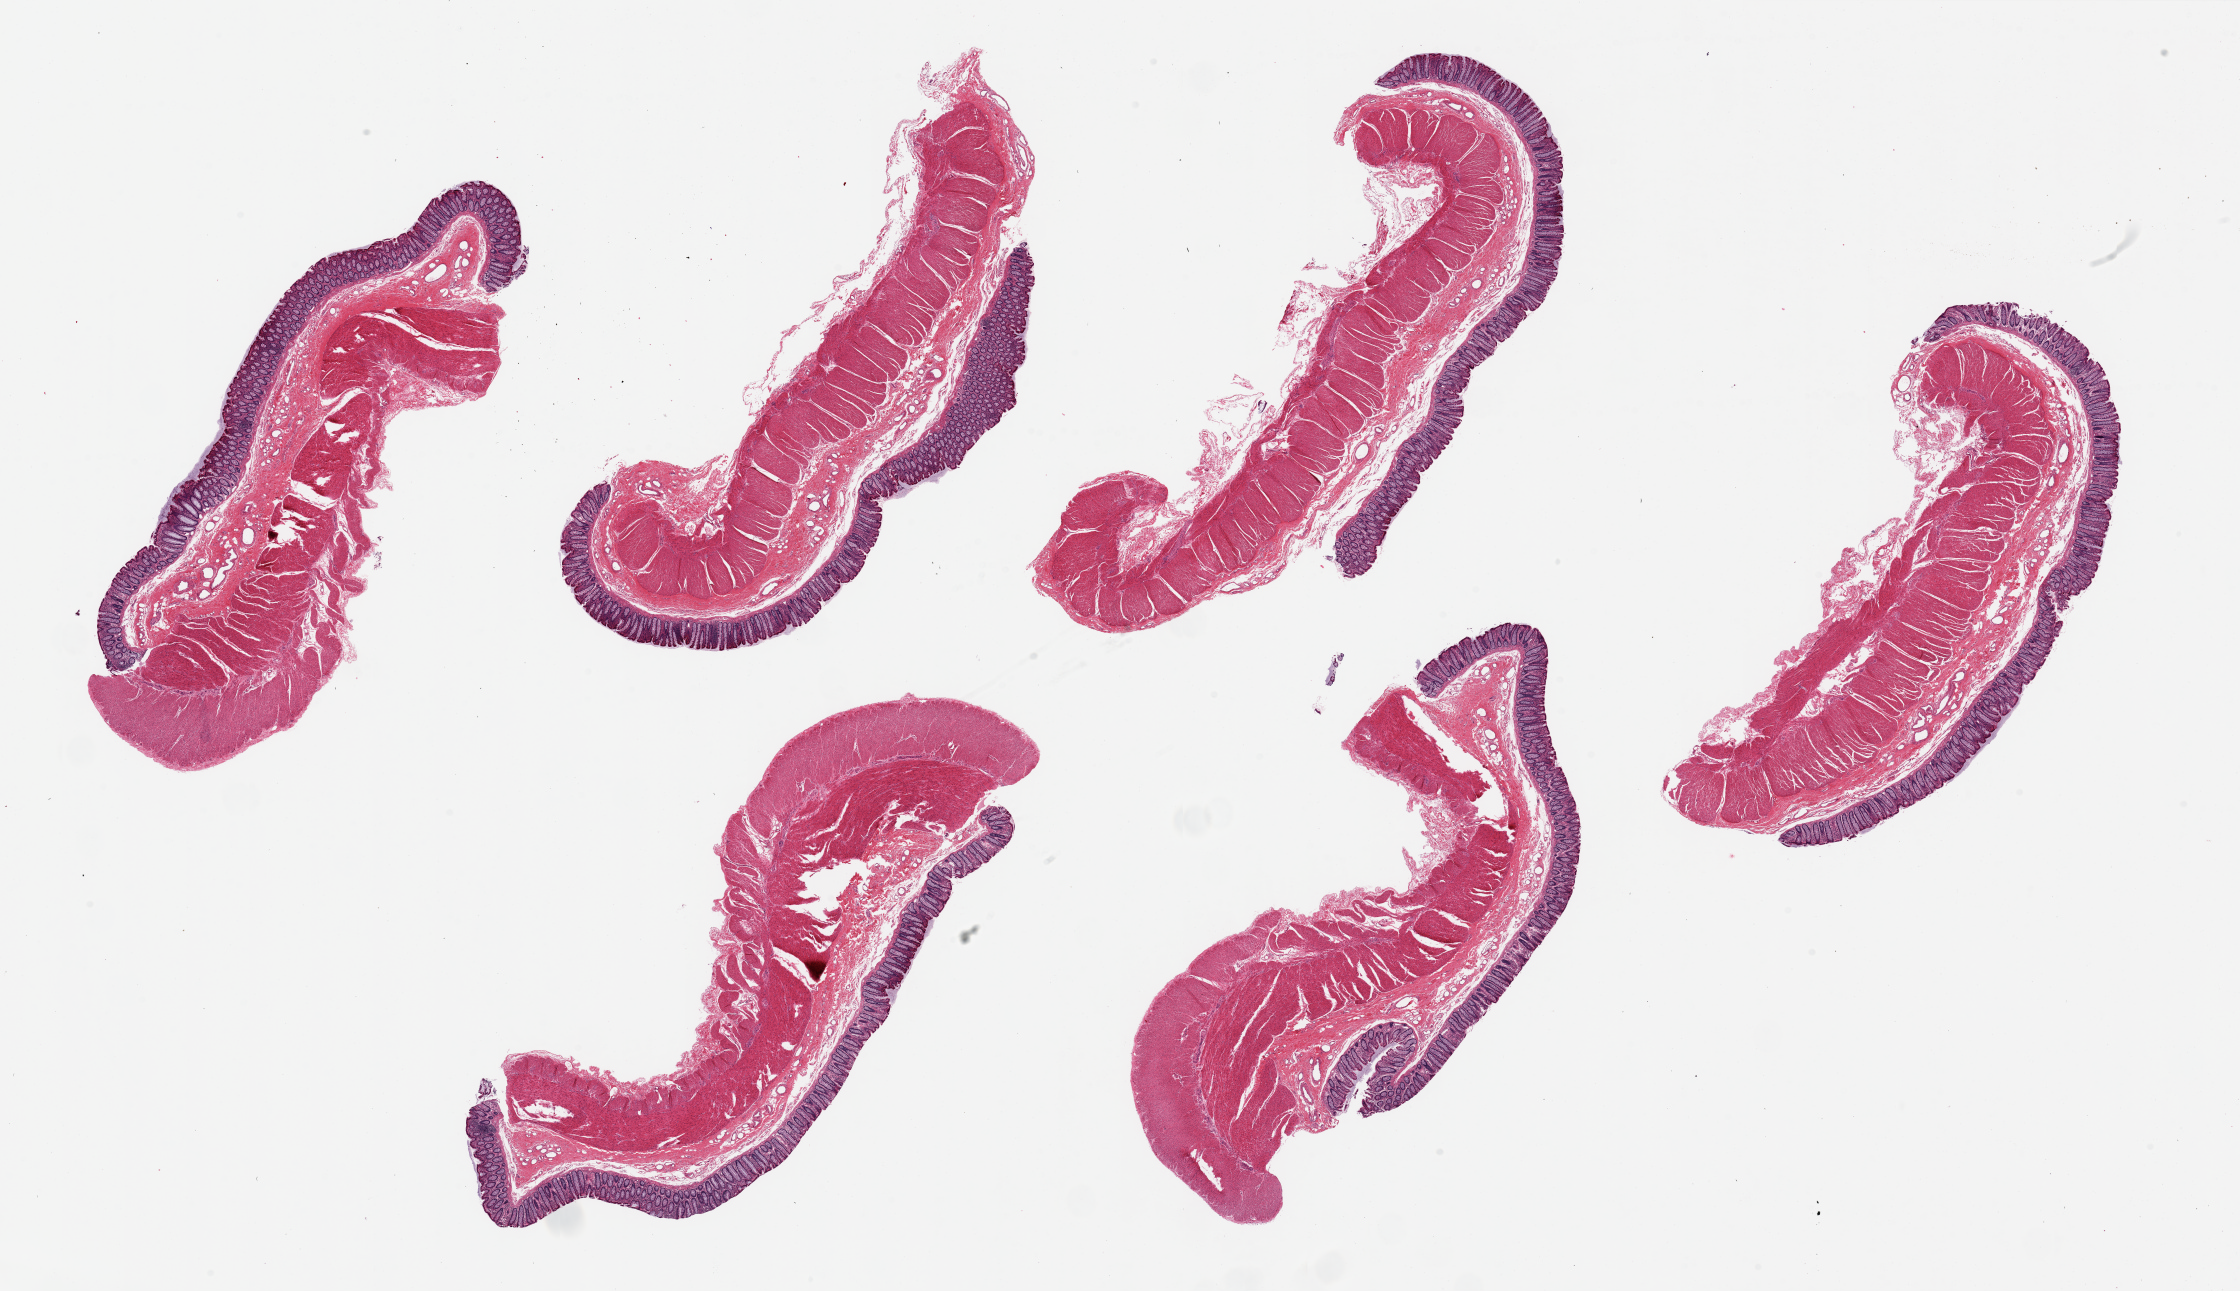
Whole-slide image, haematoxylin and eosin stain, brightfield, whole scanned area (about 35.4 x 20.4 mm) shown as a low-resolution overview, PAXgene-fixed, paraffin-embedded tissue, target tissue: transverse colon, donor tissue sample. Donor sex: male.
Reviewer comment on this tissue sample: 6 pieces, up to 11x4mm; ~20% thickness is well-preserved mucosa.